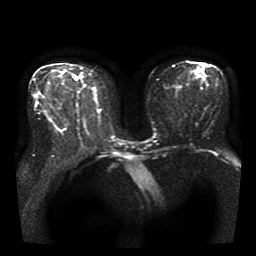
Breast MRI, one axial slice. Position 19 of 41 along the scan axis. Diffusion-weighted series; image 2 of 4 stored at this slice position (different b-values; order by instance number). 1.5 T. 256 × 256 image matrix, field of view 330 × 330 mm. Female patient.
Structures marked on this image (manually delineated by an expert):
- tumour on diffusion-weighted imaging: bounding box [x1, y1, x2, y2] px = [73, 75, 76, 78]